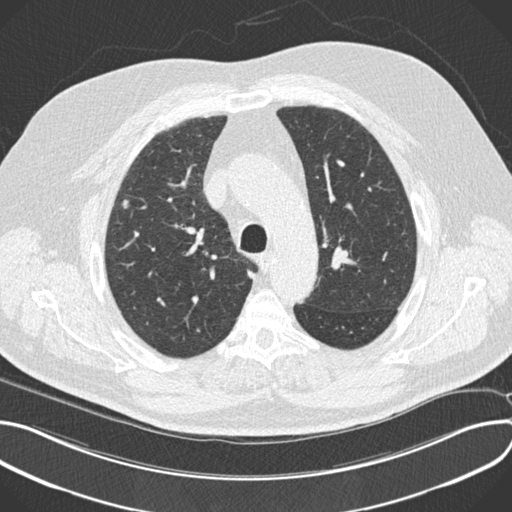
Low-dose screening chest CT, axial slice; third screening round (two years after baseline); lung window (W 1500 / L -600 HU); standard (soft-tissue) reconstruction kernel (B30f); 120 kVp; slice 56 of 212 in the series; 512 × 512 image matrix. Male participant, aged 64 years at enrolment. Current smoker at enrolment.
• Expert reader's lesion annotation, box from (x=108, y=188) to (x=143, y=224) px.
• The exam's reader record, not a measurement of the box and not confirmed to be the same lesion: non-calcified nodule or mass ≥4 mm, right upper lobe, 7 × 6 mm, smooth margins, soft tissue attenuation, pre-existing on the prior screen: no.
• Lung cancer was diagnosed 104 days after this screen: squamous cell carcinoma, NOS, right upper lobe, moderately differentiated (G2), stage IA (AJCC 6th edition), 7 mm at pathology.